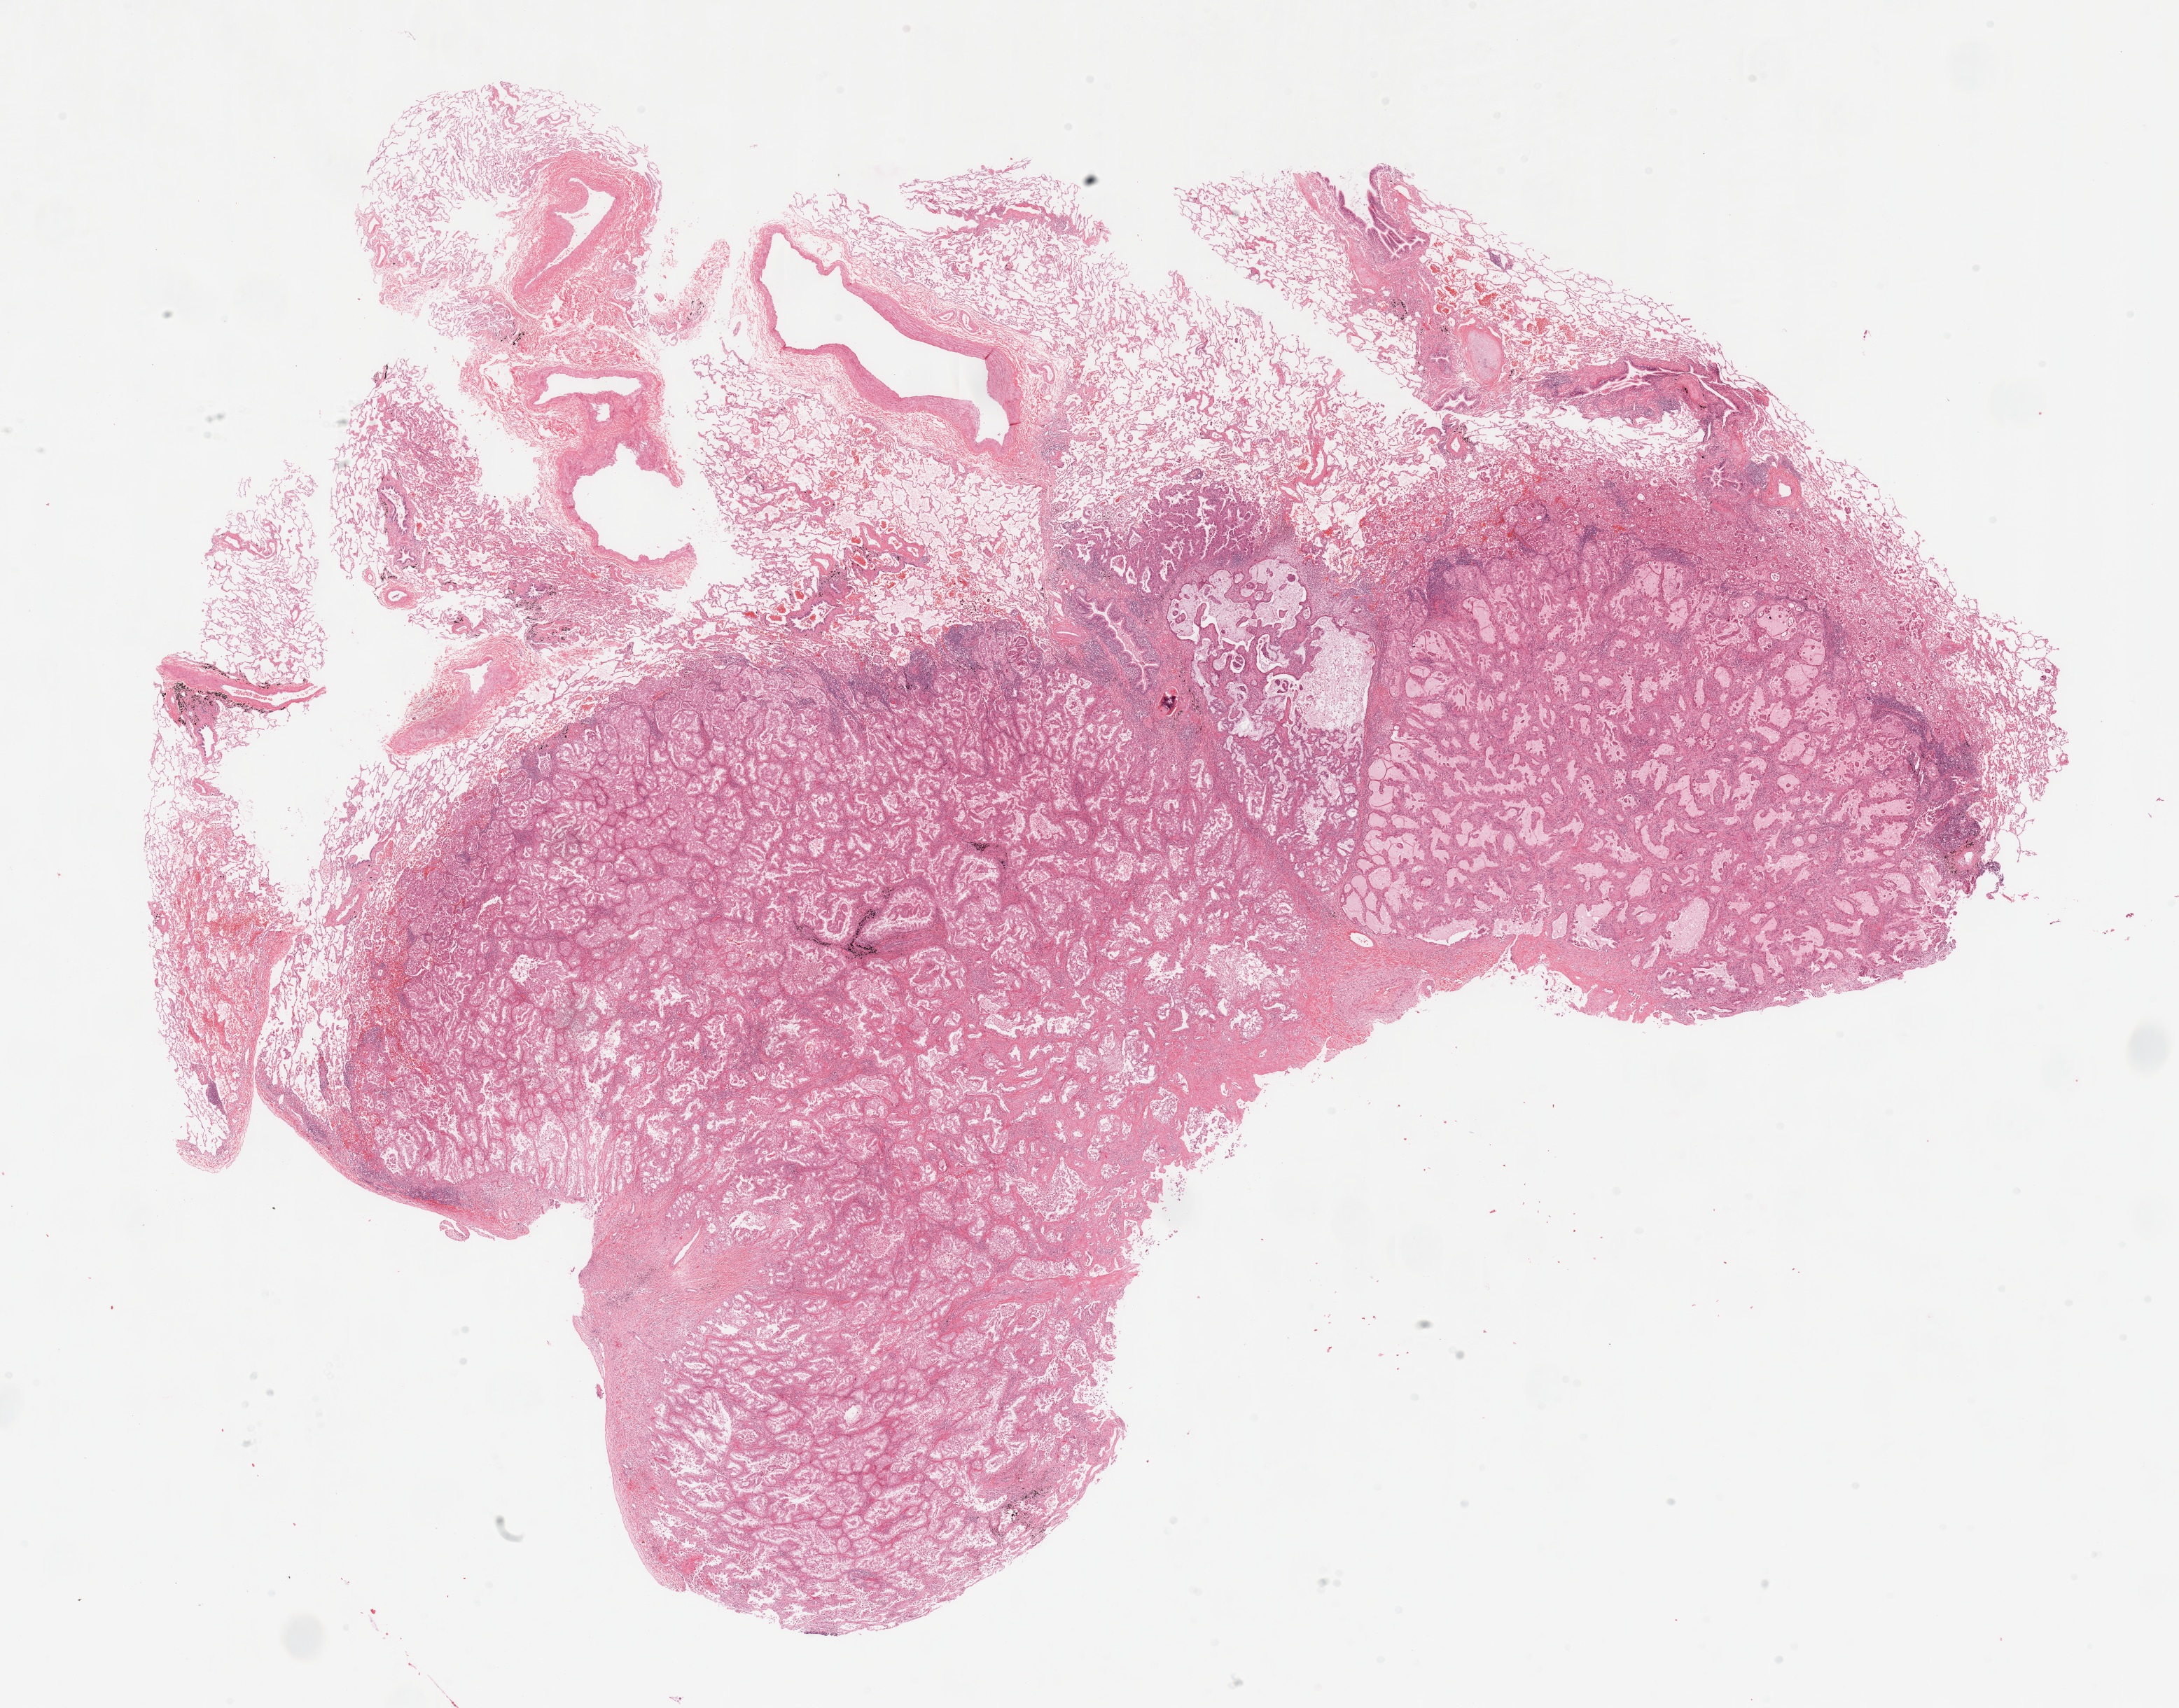
Digitized H&E tissue section (whole slide), shown as a low-resolution overview of the whole scanned area (about 24.6 x 19.3 mm), lung, tumour tissue. Female, 48 y/o. Histologic grade: G2 (moderately differentiated).
- AJCC pathologic stage: IA
- primary tumour site (as recorded): right lower lobe
- histologic diagnosis: Adenocarcinoma, NOS